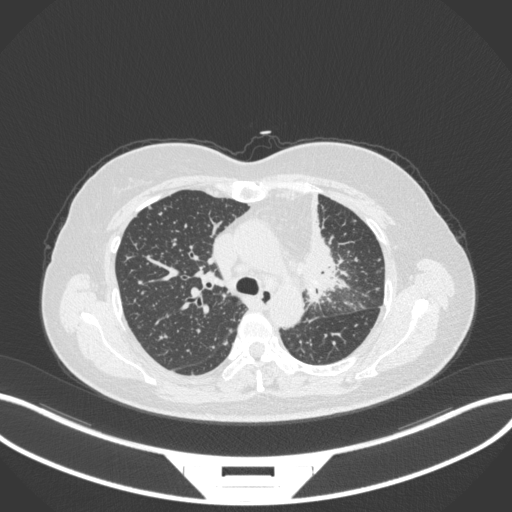
Chest CT, one axial slice. Position 228 of 348 along the scan axis. Reconstruction kernel B31f. Lung window (W 1500 / L -600 HU). 1 mm slice thickness. 512 × 512 image matrix, field of view 400 × 400 mm. Female patient, age 49 years. From the clinical record (not read from this slice): clinical TNM (as recorded): T1c N0 M1.
Annotated regions visible in this slice (rectangle marked by the reading radiologist):
- lung tumour (recorded histology: adenocarcinoma): bounding box [x1, y1, x2, y2] px = [290, 191, 354, 306]